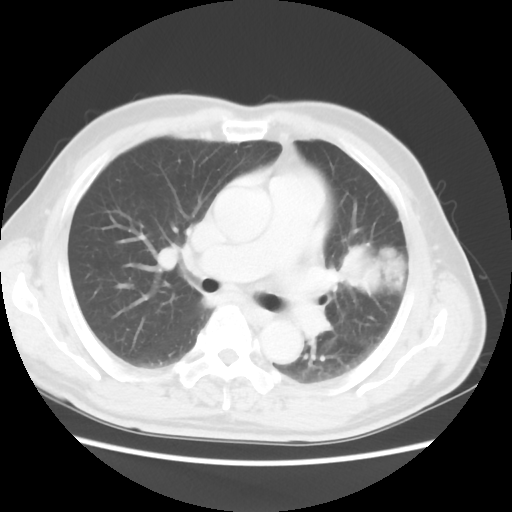
Chest CT, one axial slice; position 29 of 50 along the scan axis; reconstruction kernel STANDARD; lung window (W 1500 / L -600 HU); 512 × 512 image matrix, field of view 360 × 360 mm. Patient: male, 69 years. Case-level facts recorded for this patient, not image findings: clinical TNM (as recorded): T3 N1 M1a.
Annotated regions visible in this slice (bounding box drawn by a radiologist):
- lung tumour (recorded histology: squamous cell carcinoma): bounding box <333,236,426,309> (left, top, right, bottom; pixels)